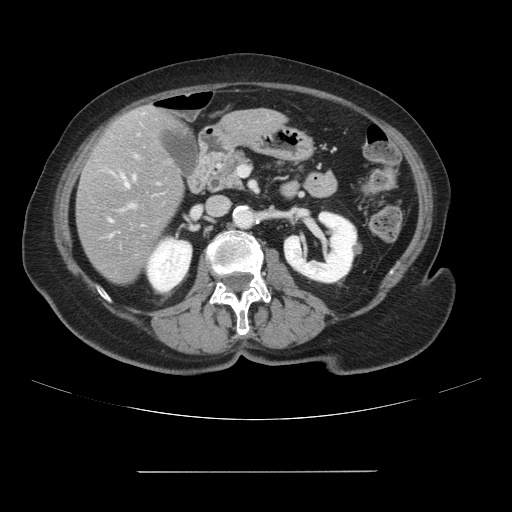
Contrast-enhanced abdominal CT, one axial slice. Position 35 of 111 along the scan axis. Soft-tissue window (W 400 / L 40 HU). 2.5 mm slice thickness. 512 × 512 image matrix, field of view 400 × 400 mm. Female patient, age 74 years. From the clinical record (not read from this slice): diagnosis: colorectal cancer liver metastases, imaged before liver resection; multiple liver metastases: yes; largest metastasis: 1.1 cm; disease in both lobes: yes.
Annotated regions visible in this slice (expert manual segmentation):
- hepatic veins: box from (x=124, y=179) to (x=128, y=186) px
- liver: (x=77, y=106)–(x=282, y=284)
- planned liver remnant (the part of the liver to remain after resection): (x=140, y=106)–(x=263, y=136)